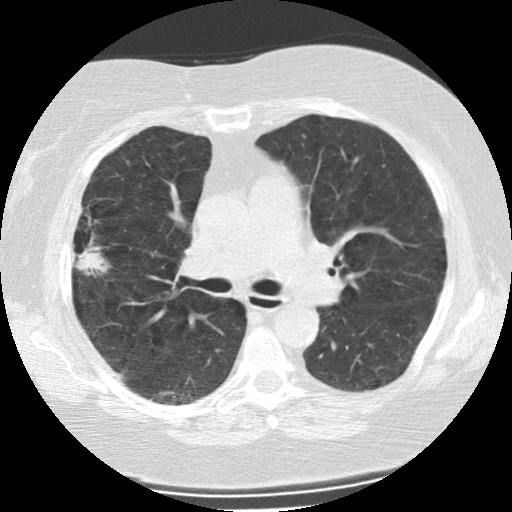
Axial slice from a low-dose chest CT screening exam. Second screening round (one year after baseline). Lung window (W 1500 / L -600 HU). 2.5 mm slice thickness. 512 × 512 image matrix. Female participant, aged 73 years at enrolment. Former smoker at enrolment.
Lesion marked by an expert reader, bounding box [x1, y1, x2, y2] px = [55, 212, 110, 284]. The screening reader recorded 2 non-calcified nodules or masses ≥4 mm on this exam (right upper lobe, left upper lobe); which of them this box marks is not recorded. Later outcome: lung cancer diagnosed 47 days after this screen — bronchiolo-alveolar adenocarcinoma, NOS, right upper lobe, moderately differentiated (G2), stage IIIB (AJCC 6th edition), 21 mm at pathology.